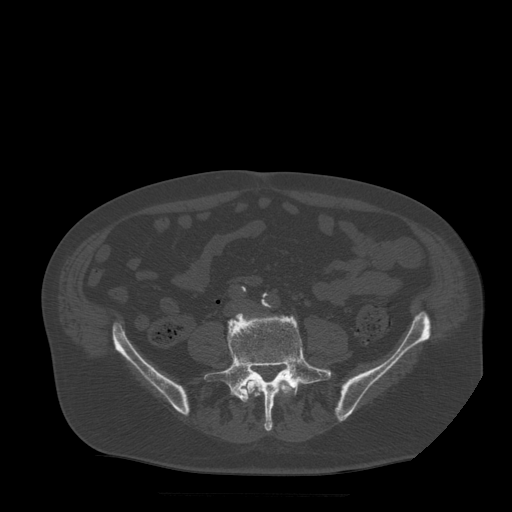
CT including the spine, one axial slice. Position 94 of 522 along the scan axis. Bone window (W 1800 / L 400 HU). 1.25 mm slice thickness. 512 × 512 image matrix, field of view 420 × 420 mm. Patient age 72 years. From the clinical record (not read from this slice): primary cancer: prostate.
Structures marked on this image (semi-automatic segmentation, software-assisted and operator-edited):
- L4 vertebra: box from (x=241, y=378) to (x=296, y=402) px
- L5 vertebra: (x=204, y=313)–(x=332, y=432)